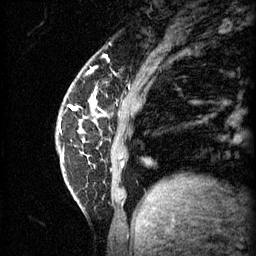
Breast MRI (dynamic contrast-enhanced), one sagittal slice. Position 10 of 60 along the scan axis. 3 images stored at this slice position (order not interpretable as contrast timing). 1.5 T. TE 4.2 ms, TR 11 ms. 2 mm slice thickness. 256 × 256 image matrix. Female patient, age 62 years.
Annotated regions visible in this slice (semi-automatic segmentation, software-assisted and operator-edited):
- analysis volume of interest (the breast-tissue region the enhancement analysis was run in; not a lesion): bounding box <58,76,101,135> (left, top, right, bottom; pixels)
- tumour enhancement mask (voxels above the 70 % enhancement threshold inside the analysis volume of interest): <76,100,96,111>